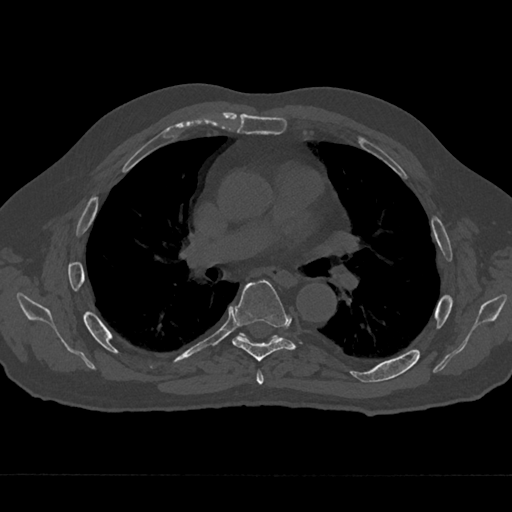
CT including the spine, one axial slice. Reconstruction kernel Br40s/3. Bone window (W 1800 / L 400 HU). 0.5 mm slice thickness. 512 × 512 image matrix, field of view 377 × 377 mm. Male patient, age 75 years. Case-level facts recorded for this patient, not image findings: primary cancer: renal.
Structures marked on this image (semi-automatically segmented with operator editing):
- T5 vertebra: box from (x=256, y=370) to (x=264, y=385) px
- T6 vertebra: (x=232, y=280)–(x=302, y=362)
- T7 vertebra: (x=242, y=334)–(x=276, y=337)